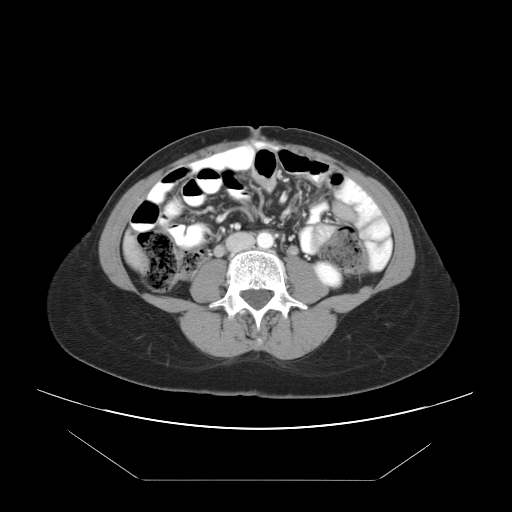
Contrast-enhanced abdominal CT, one axial slice. Slice 6 of 45 in the series (ordered by position). Reconstruction kernel STANDARD. Intravenous contrast given. Soft-tissue window (W 400 / L 40 HU). 5 mm slice thickness. 512 × 512 image matrix, field of view 405 × 405 mm. Female patient, age 52 years. From the clinical record (not read from this slice): diagnosis: colorectal cancer liver metastases, imaged before liver resection; multiple liver metastases: yes; largest metastasis: 2.5 cm; disease in both lobes: no.
Outlined on this slice (manually delineated by an expert):
- liver: bounding box (x1, y1, x2, y2) in pixels: (128, 243, 143, 266)
- planned liver remnant (the part of the liver to remain after resection): (128, 243, 138, 261)